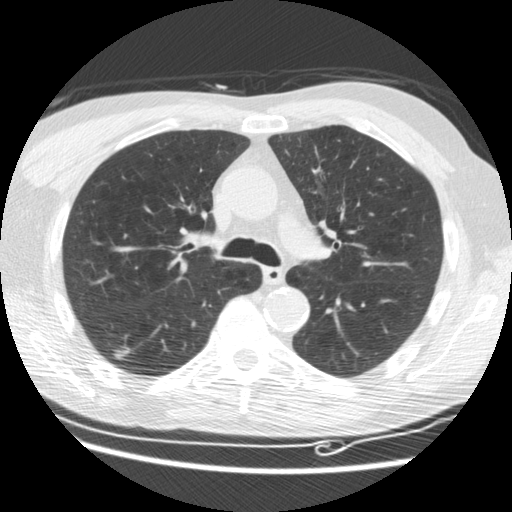
Axial slice from a low-dose chest CT screening exam; third screening round (two years after baseline); lung window (W 1500 / L -600 HU); standard (soft-tissue) reconstruction kernel (STANDARD); slice 64 of 176 in the series; 512 × 512 image matrix. Male, age 62 years at enrolment. Current smoker at enrolment.
Expert-annotated lung lesion, bounding box (x1, y1, x2, y2) in pixels: (103, 335, 141, 368). The screening reader recorded 3 non-calcified nodules or masses ≥4 mm on this exam (right lower lobe, right lower lobe, right lower lobe); which of them this box marks is not recorded. Official screen result: positive, other. Lung cancer was diagnosed 33 days after this screen: adenocarcinoma, NOS, right lower lobe, moderately differentiated (G2), stage IIIB (AJCC 6th edition), 15 mm at pathology.